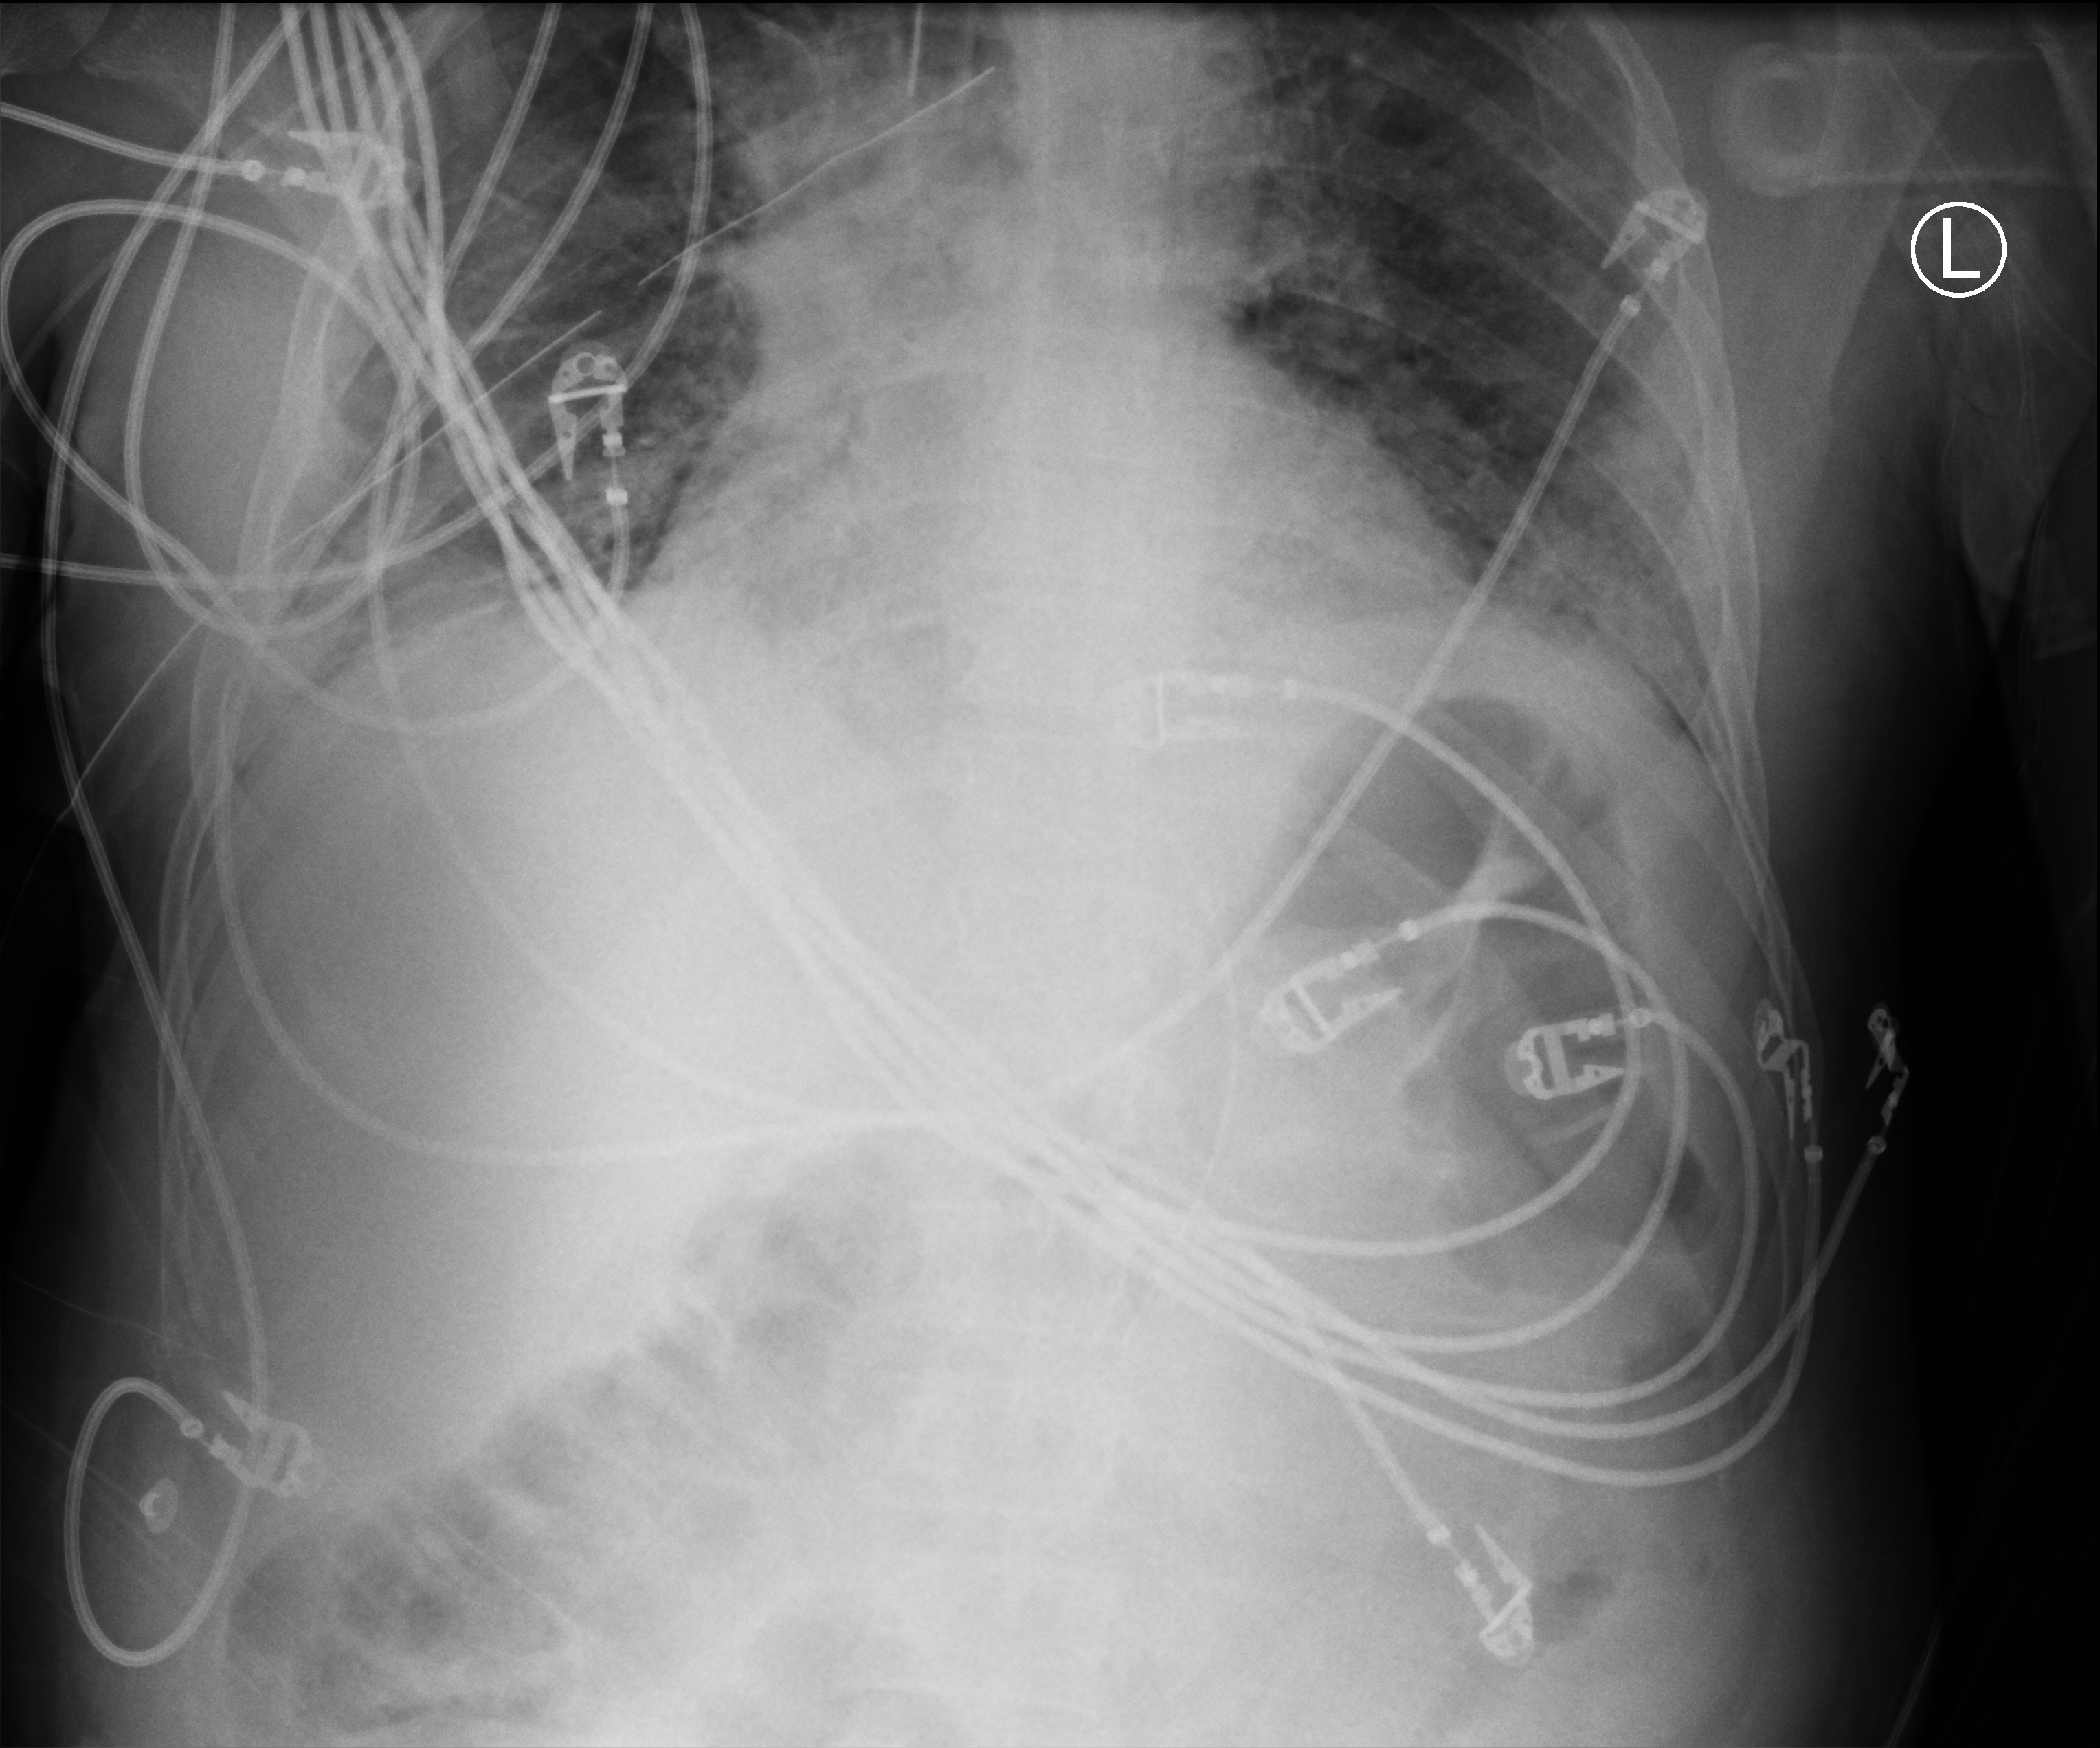
Portable chest radiograph; anteroposterior (AP) projection. Male patient hospitalised with COVID-19, age 18–59 years.
From the hospital-stay record, not from the radiograph (when in the stay this image was taken is not recorded): mechanically ventilated during this hospital stay: yes; admitted to intensive care during this hospital stay: yes.